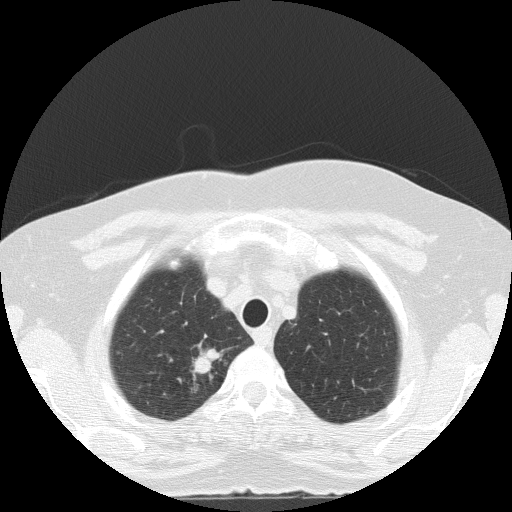
Low-dose screening chest CT, one axial slice; slice 115 of 133 in the series (ordered by position); reconstruction kernel FC51; lung window (W 1500 / L -600 HU); 2 mm slice thickness; 512 × 512 image matrix.
Outlined on this slice (expert manual segmentation):
- lesion 1 (tumor, upper lobe of right lung): bounding box (x1, y1, x2, y2) in pixels: (192, 348, 222, 381)